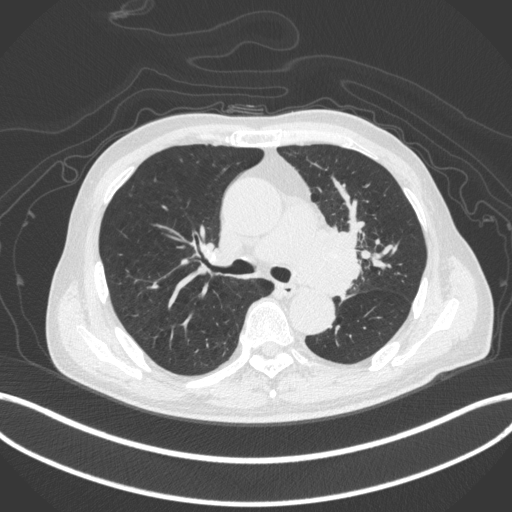
Chest CT, one axial slice. Position 273 of 420 along the scan axis. Reconstruction kernel B31f. Lung window (W 1500 / L -600 HU). 1 mm slice thickness. 512 × 512 image matrix. Male patient, age 77 years. From the clinical record (not read from this slice): clinical TNM (as recorded): T3 N1 M0.
Outlined on this slice (bounding box drawn by a radiologist):
- lung tumour (recorded histology: adenocarcinoma): bounding box (x1, y1, x2, y2) in pixels: (296, 223, 361, 302)